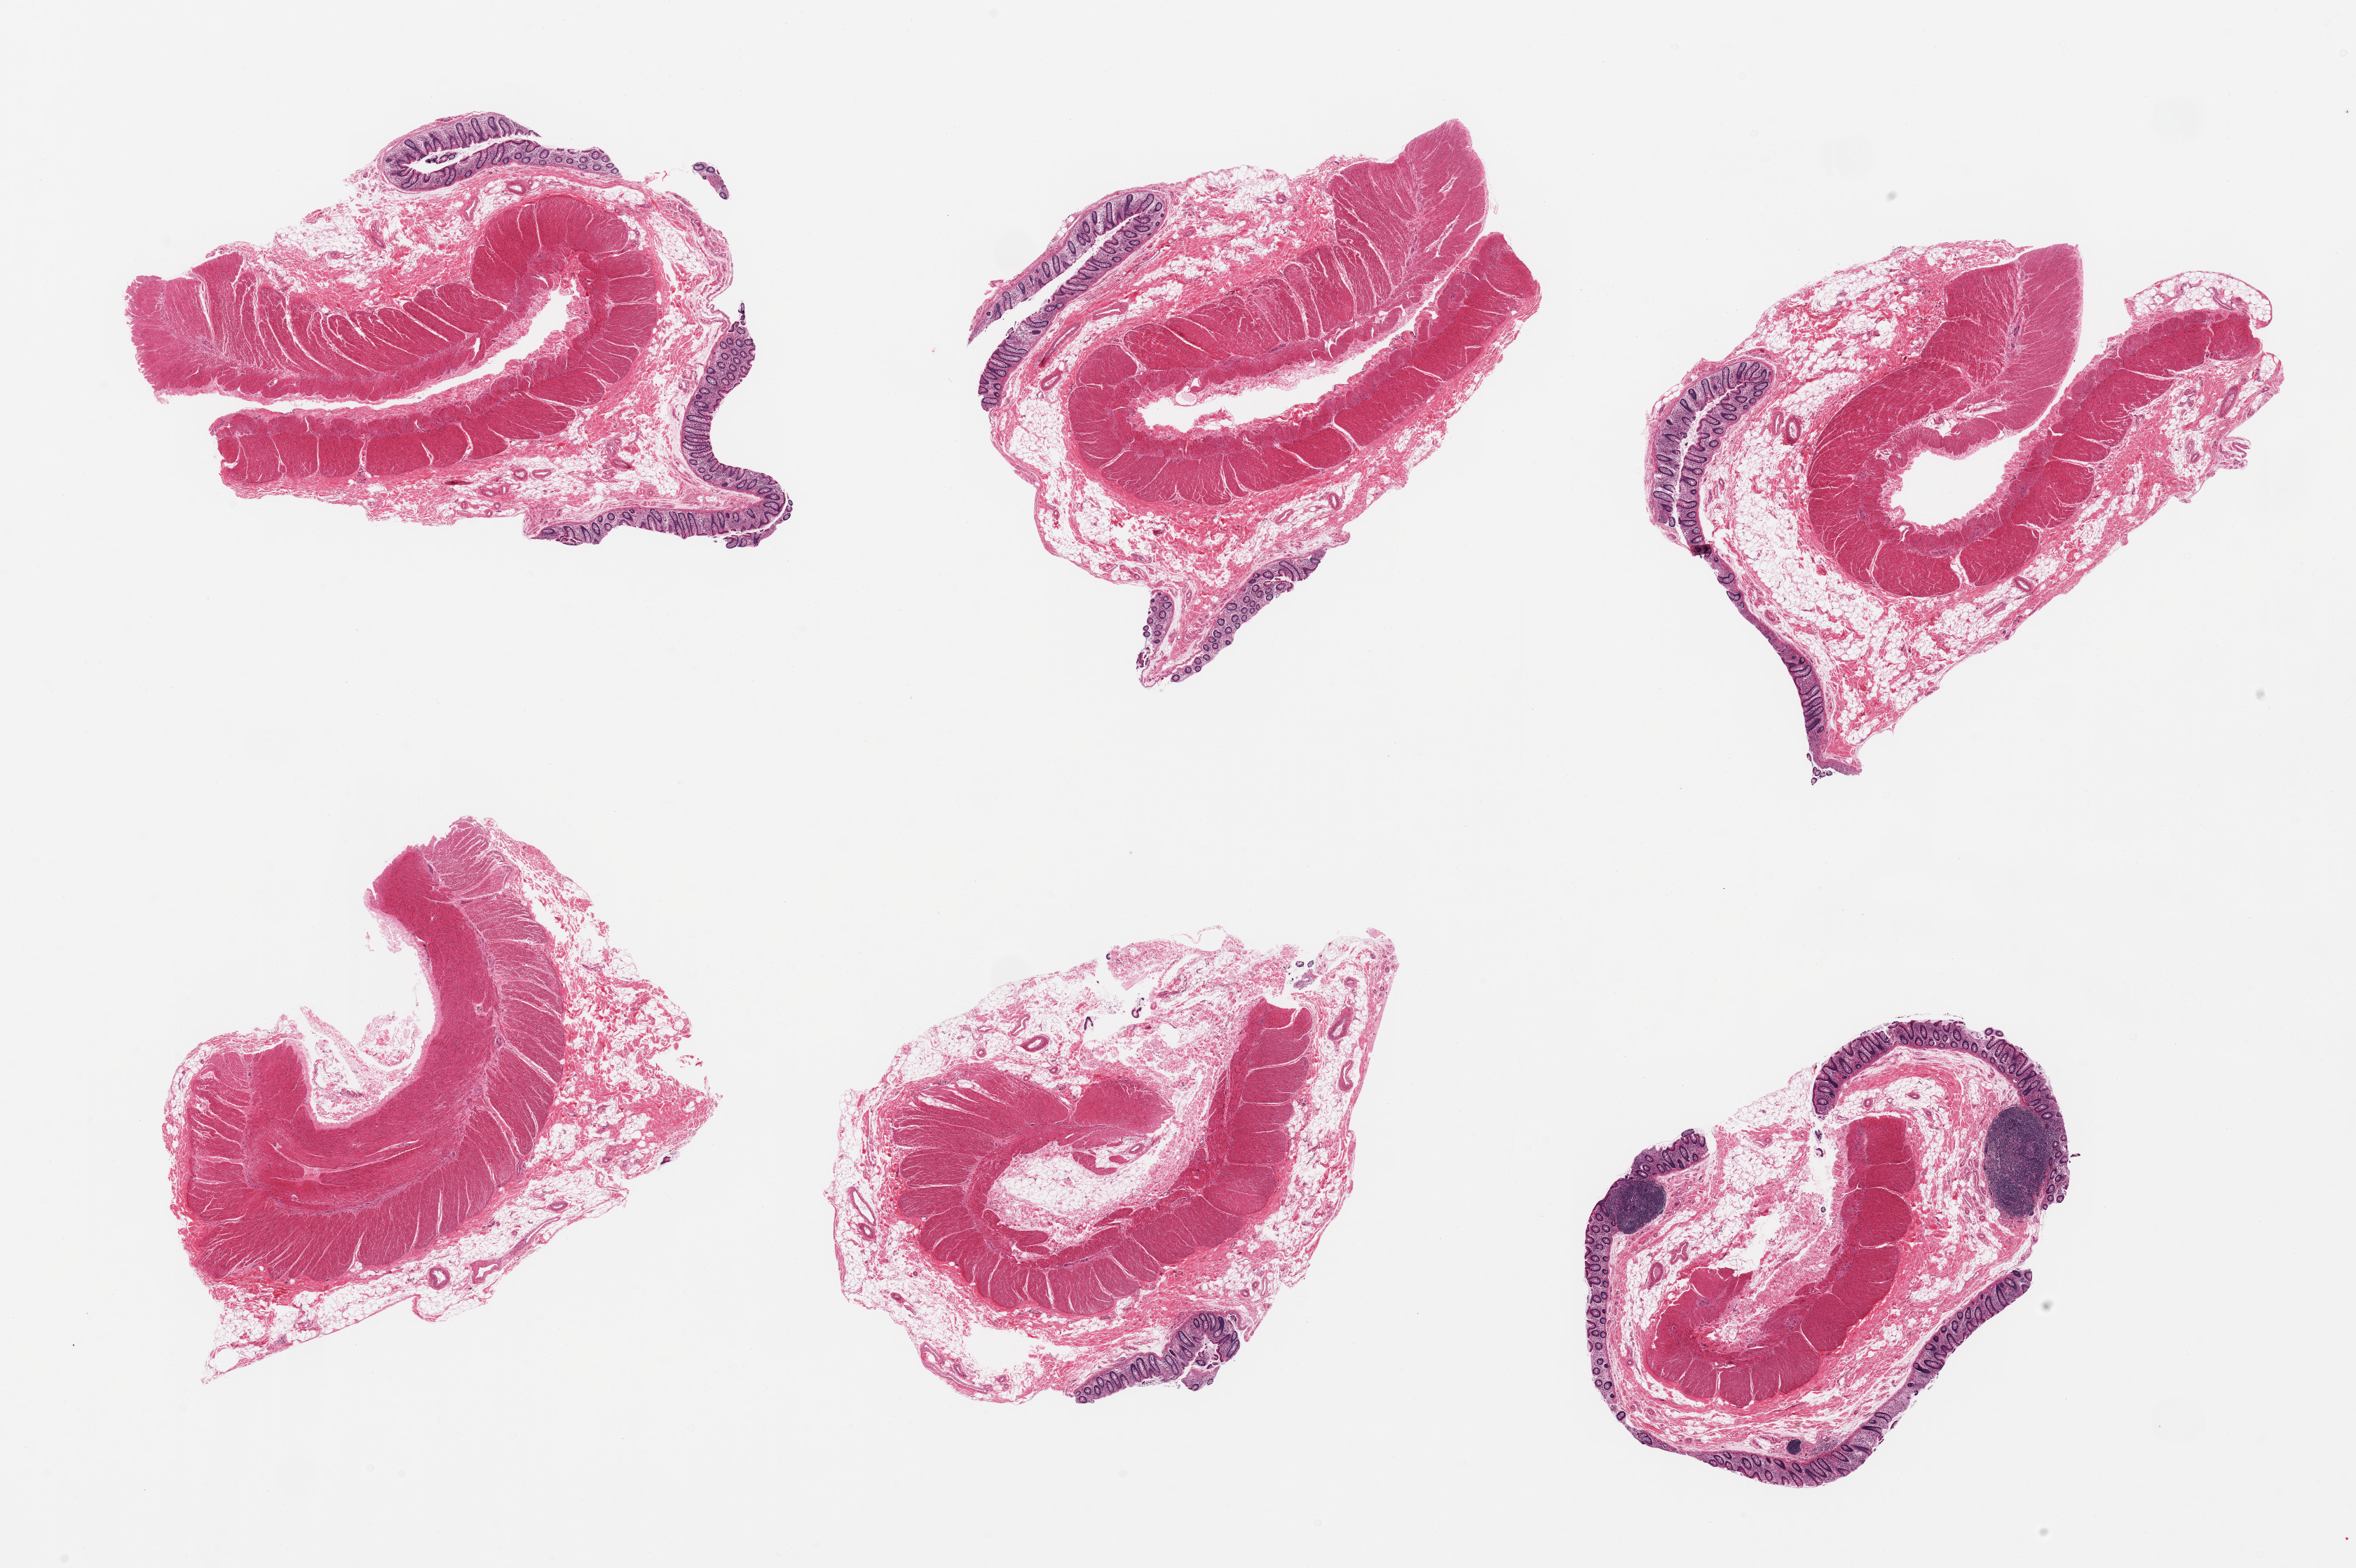
Whole-slide image, haematoxylin and eosin stain, a low-resolution overview of the entire scanned area, about 26.6 x 17.7 mm (acquisition: 20x scan), PAXgene-fixed paraffin-embedded (PFPE) section, sampled site (target tissue): transverse colon, tissue donor sample. Male donor.
Pathologist's review note for this sample: 6 pieces, target mucosa well-fixed, partially stripped, 0.4mm, ~10-20% of thickness.